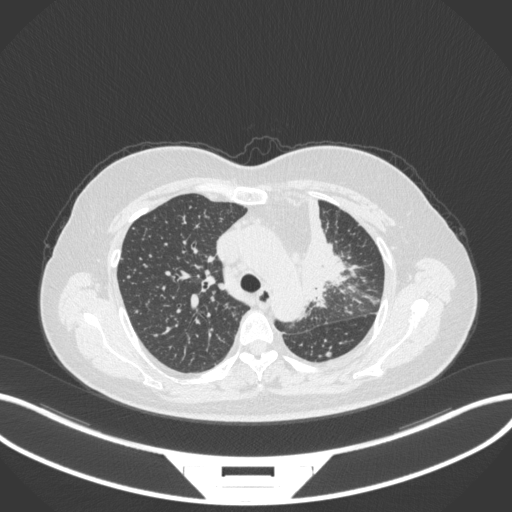
Chest CT, one axial slice; slice 238 of 348 in the series (ordered by position); lung window (W 1500 / L -600 HU); 1 mm slice thickness; 512 × 512 image matrix, field of view 400 × 400 mm. Patient: female, 49 years. Case-level facts recorded for this patient, not image findings: clinical TNM (as recorded): T1c N0 M1.
Structures marked on this image (rectangle marked by the reading radiologist):
- lung tumour (recorded histology: adenocarcinoma): bounding box [x1, y1, x2, y2] px = [298, 187, 354, 311]